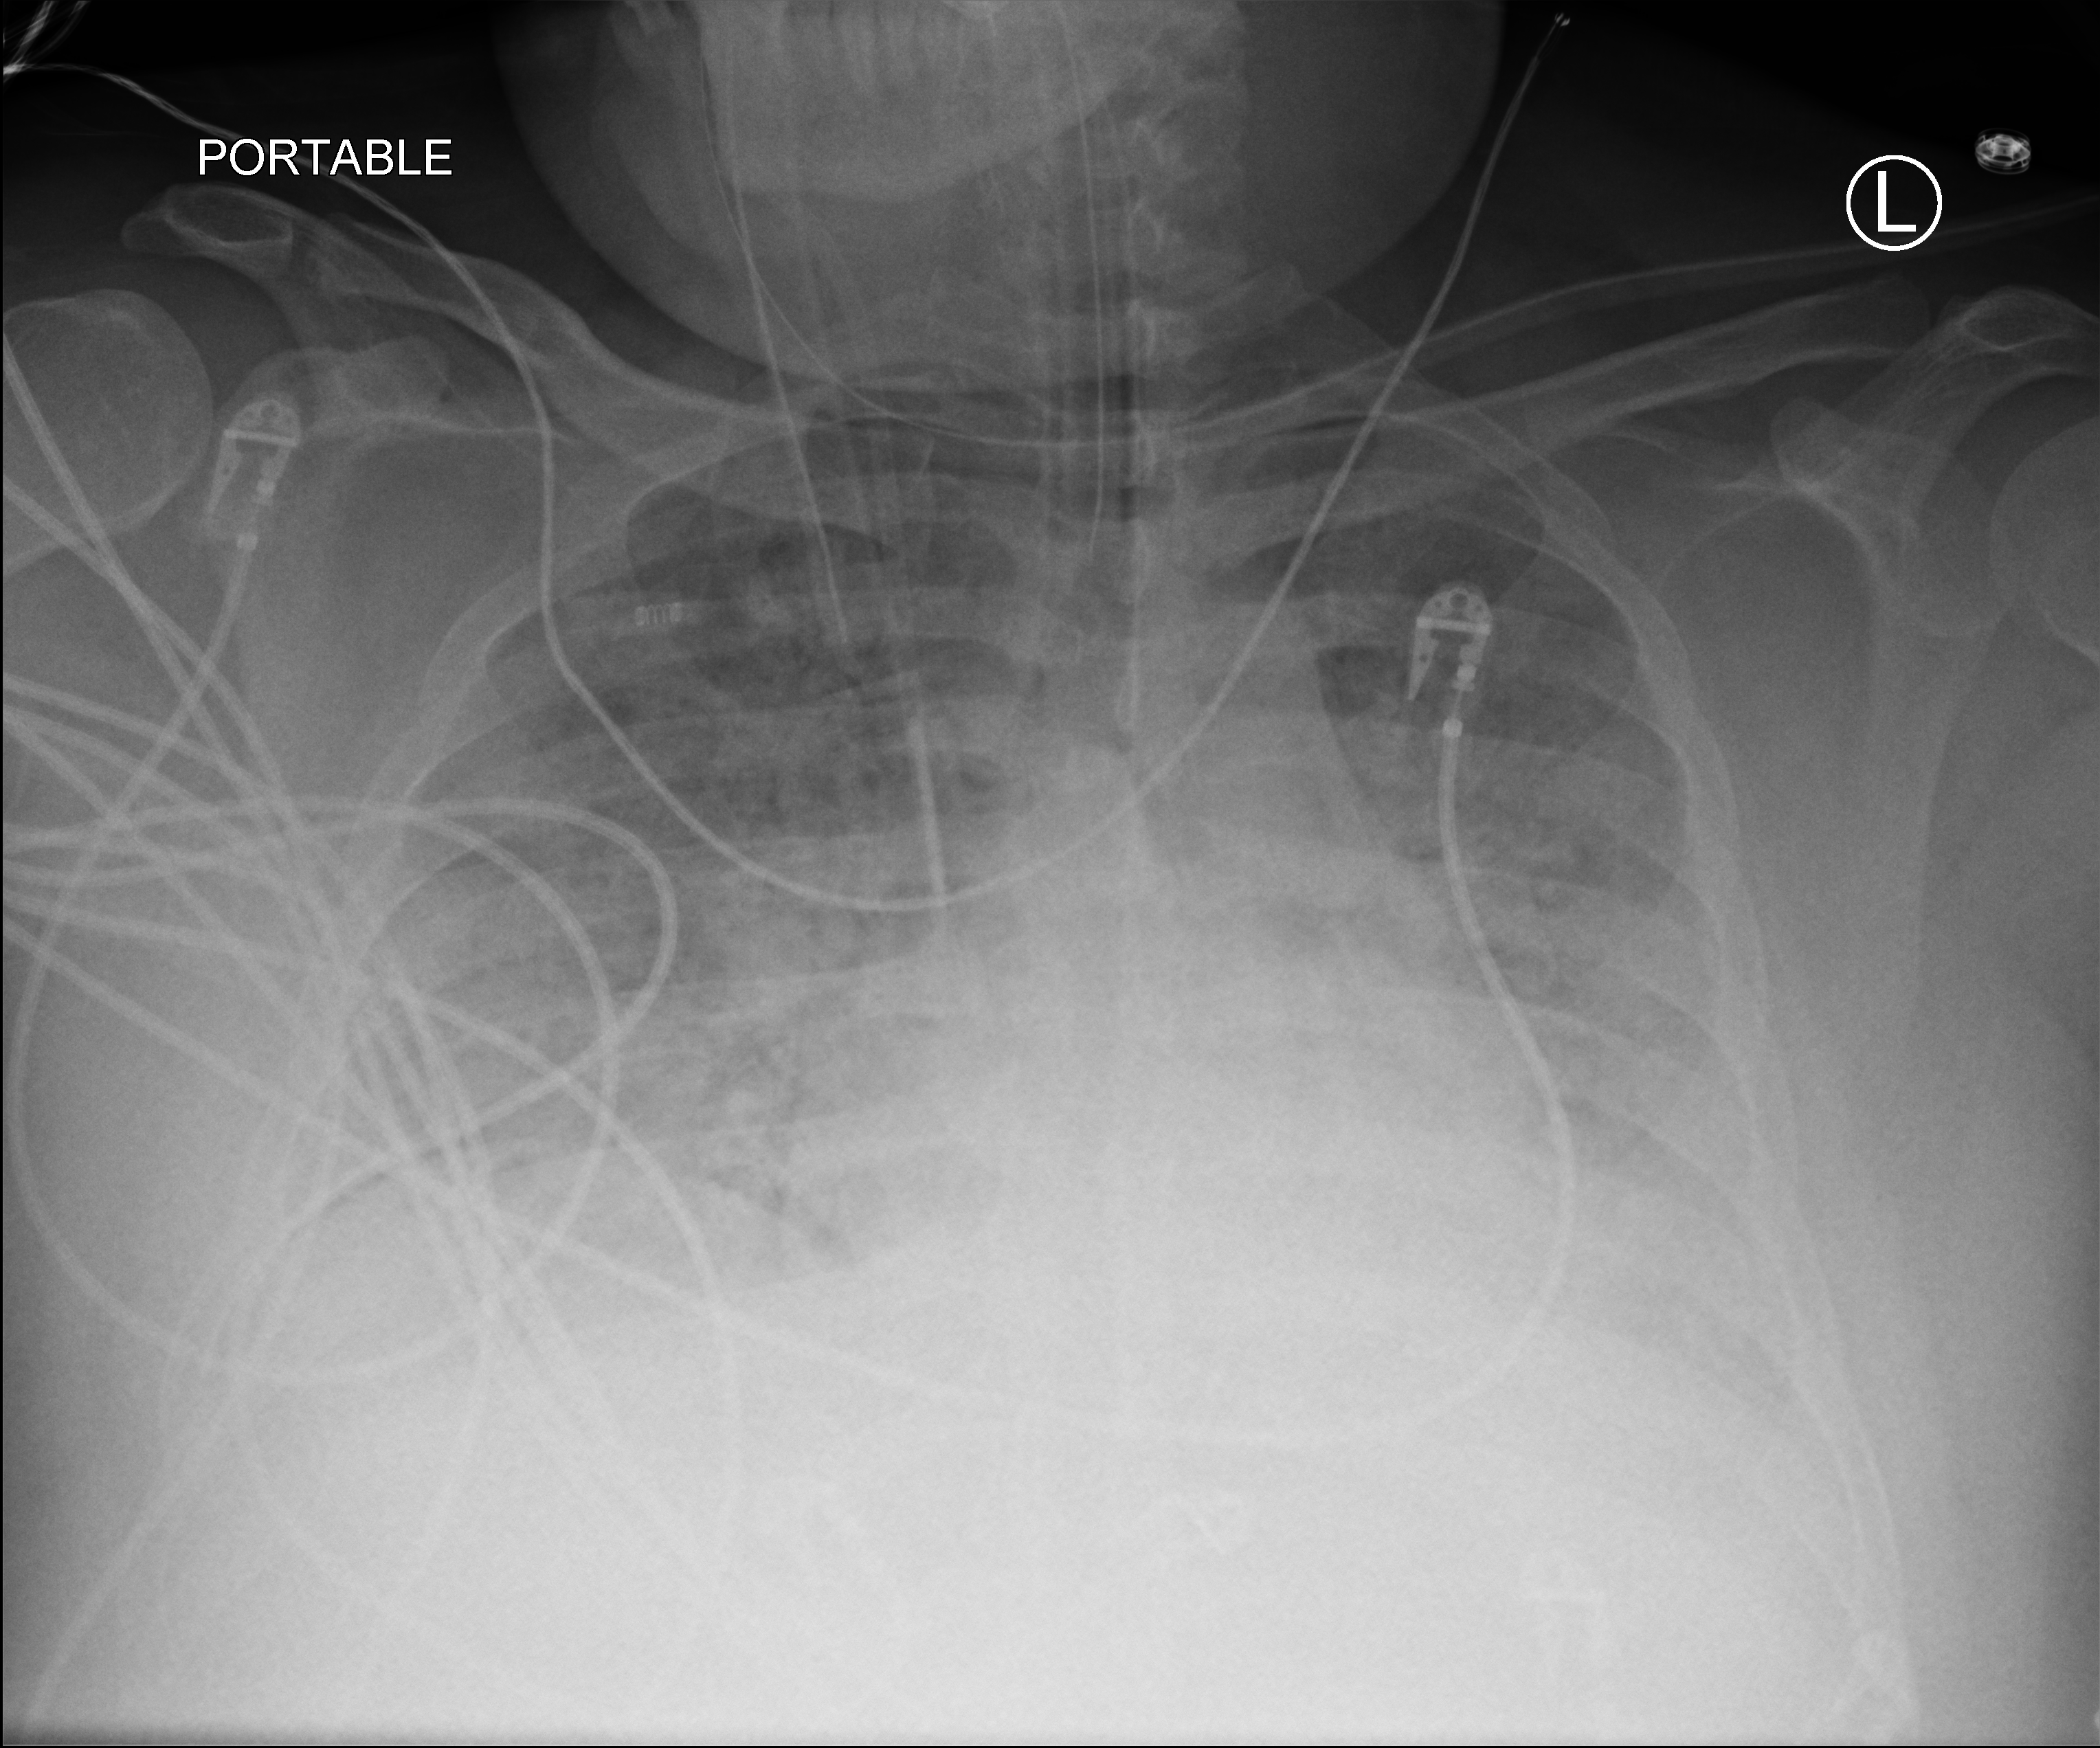
Bedside chest radiograph (computed radiography), anteroposterior (AP) projection. Patient hospitalised with COVID-19, aged 18–59 years.
From the hospital-stay record, not from the radiograph (when in the stay this image was taken is not recorded): chronic kidney disease (admission record): no; mechanically ventilated during this hospital stay: yes; COPD (admission record): no.